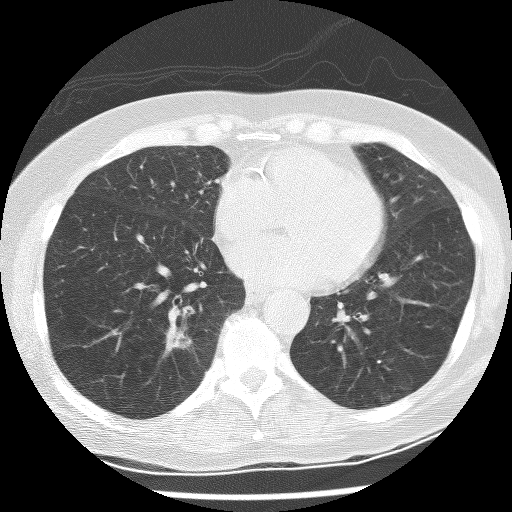
Axial slice from a low-dose chest CT screening exam. Baseline annual screen. Lung window (W 1500 / L -600 HU). Lung (sharp) reconstruction kernel (BONE). 512 × 512 image matrix, field of view 300 × 300 mm. Female, age 60 years at enrolment. Former smoker at enrolment.
Expert reader's lesion annotation, bounding box <156,322,203,358> (left, top, right, bottom; pixels). The exam's reader record, not a measurement of the box and not confirmed to be the same lesion: non-calcified nodule or mass ≥4 mm, right lower lobe, 10 × 6 mm, spiculated (stellate) margins, mixed attenuation. Later outcome: lung cancer diagnosed 275 days after this screen — adenocarcinoma with squamous metaplasia, right lower lobe, poorly differentiated (G3), stage IA (AJCC 6th edition), 23 mm at pathology.